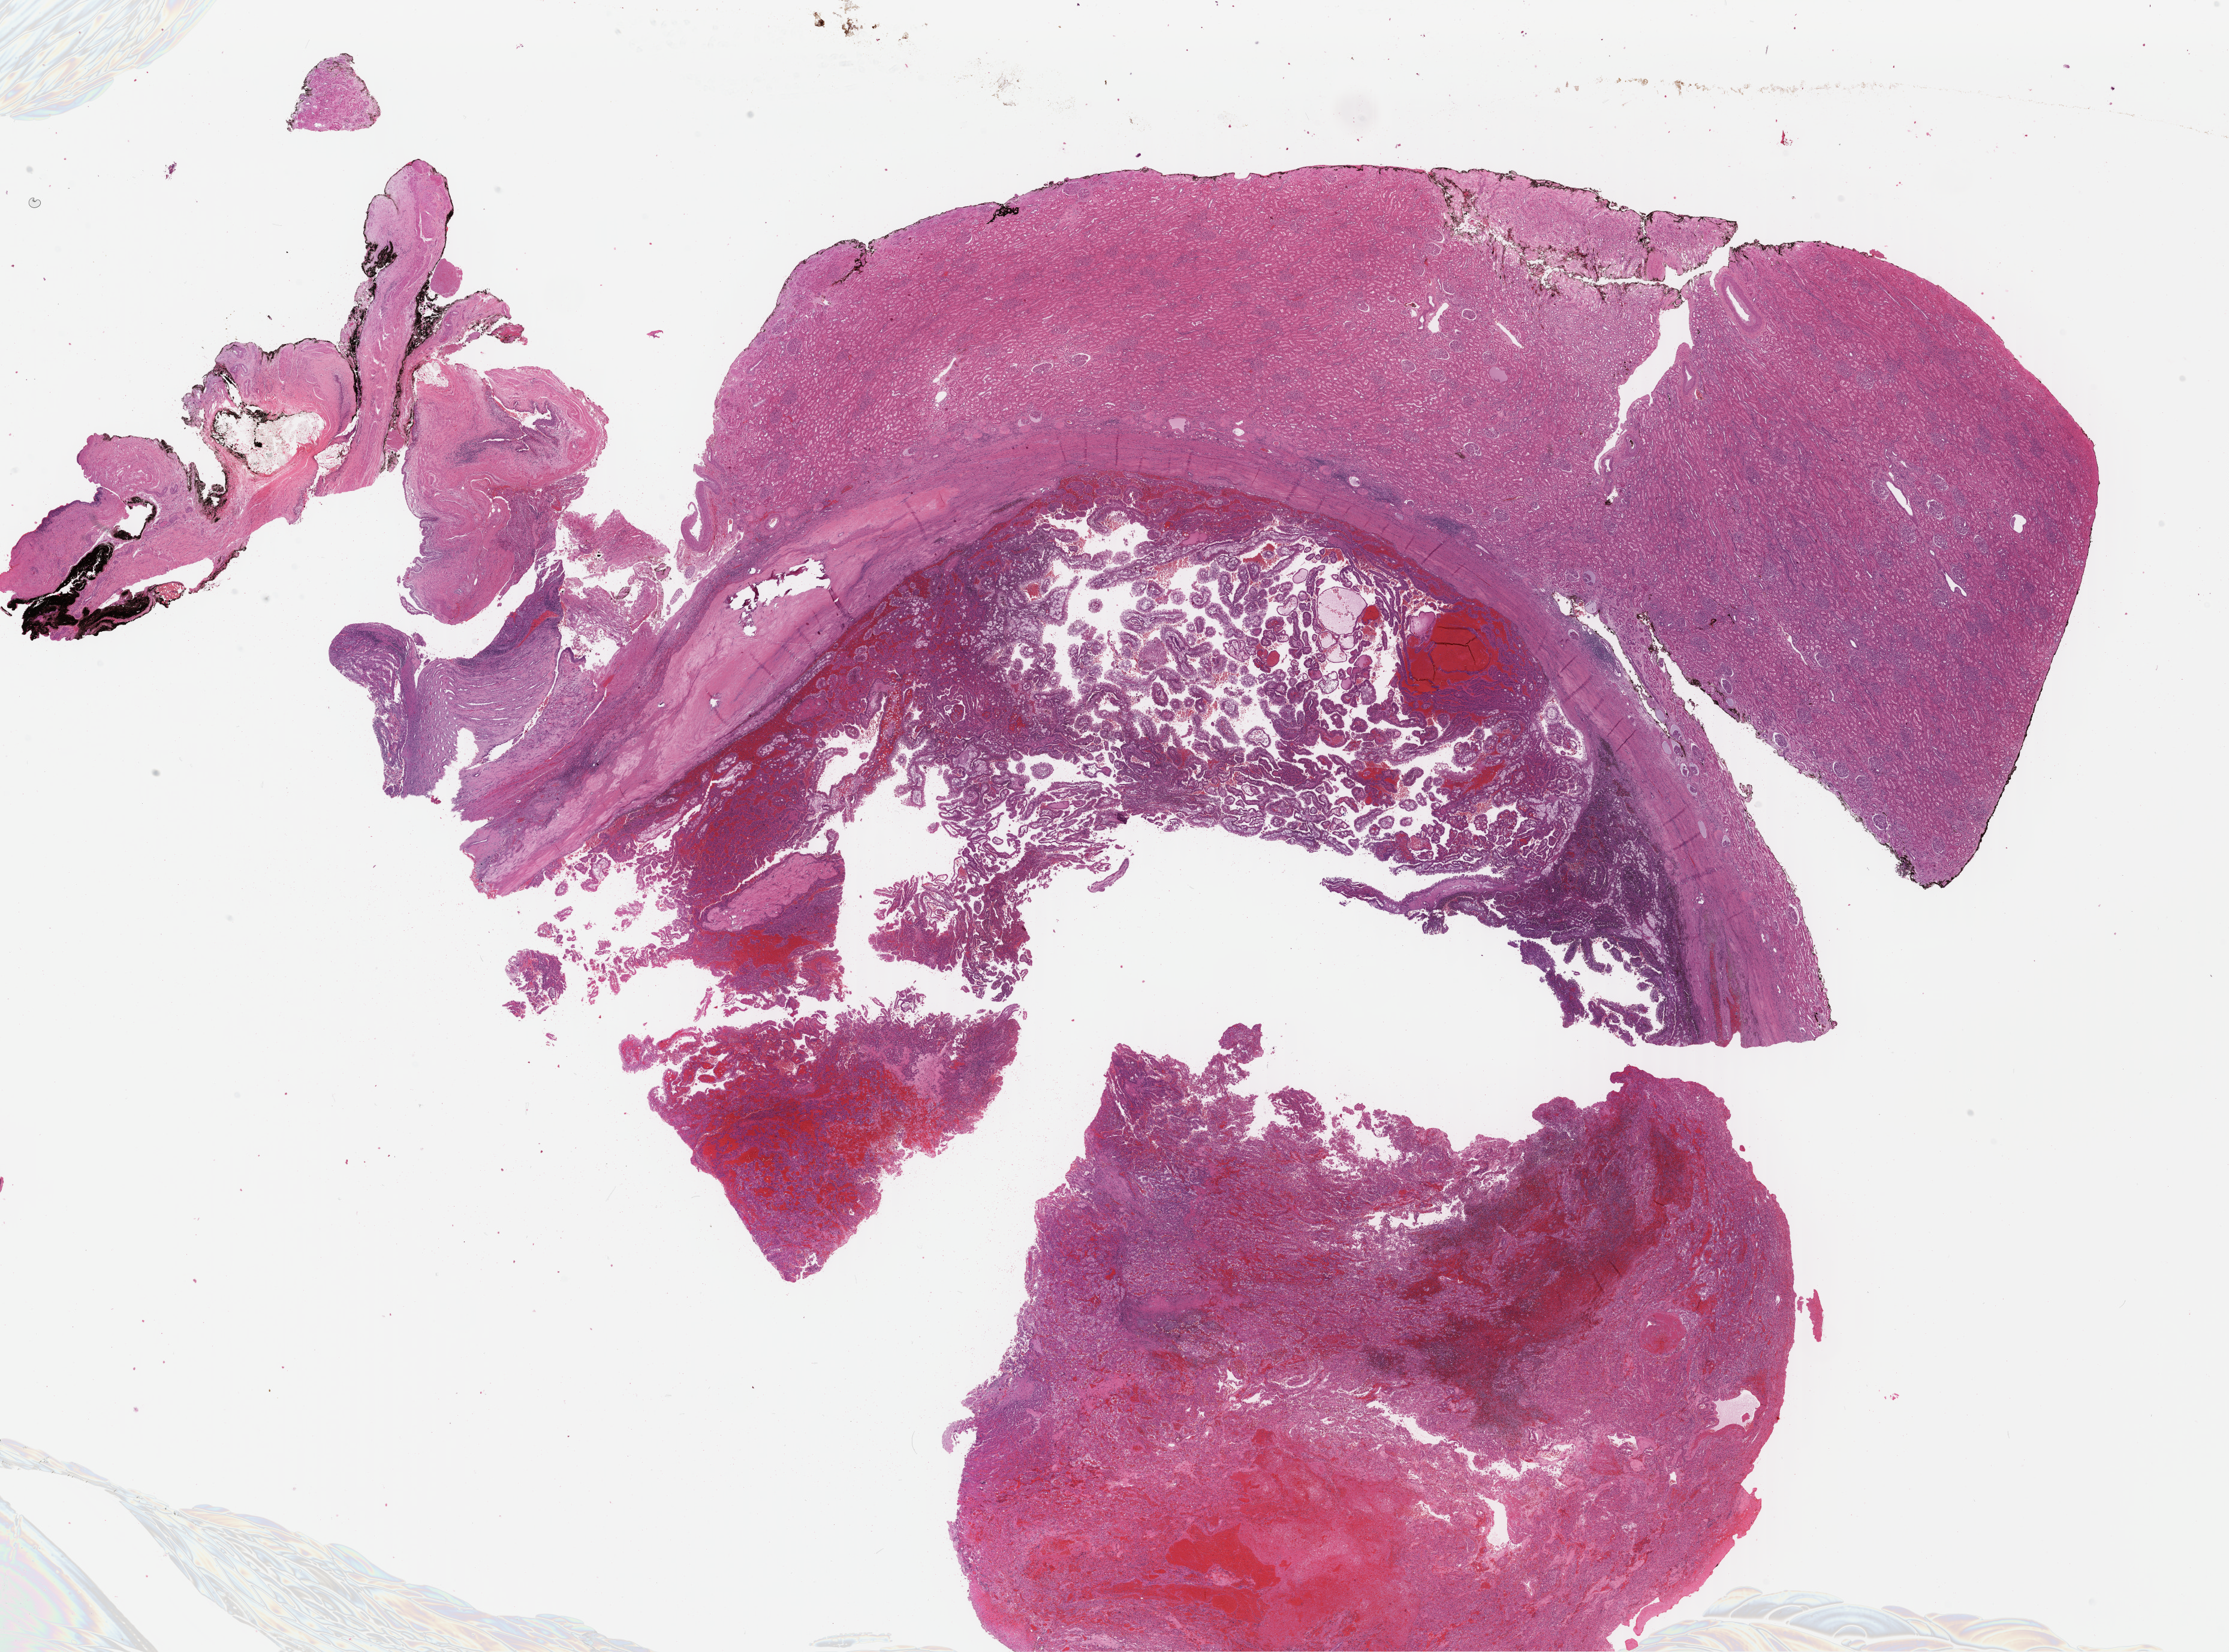
H&E whole-slide image — shown as a low-resolution overview of the whole scanned area (about 29.2 x 21.7 mm). FFPE section. Primary tumour sample from the kidney. Male, age 43 years at initial diagnosis.
- histologic diagnosis: Papillary adenocarcinoma, NOS
- lymph nodes positive (case pathology): 0 of 2 examined
- AJCC pathologic stage: I (7th edition)